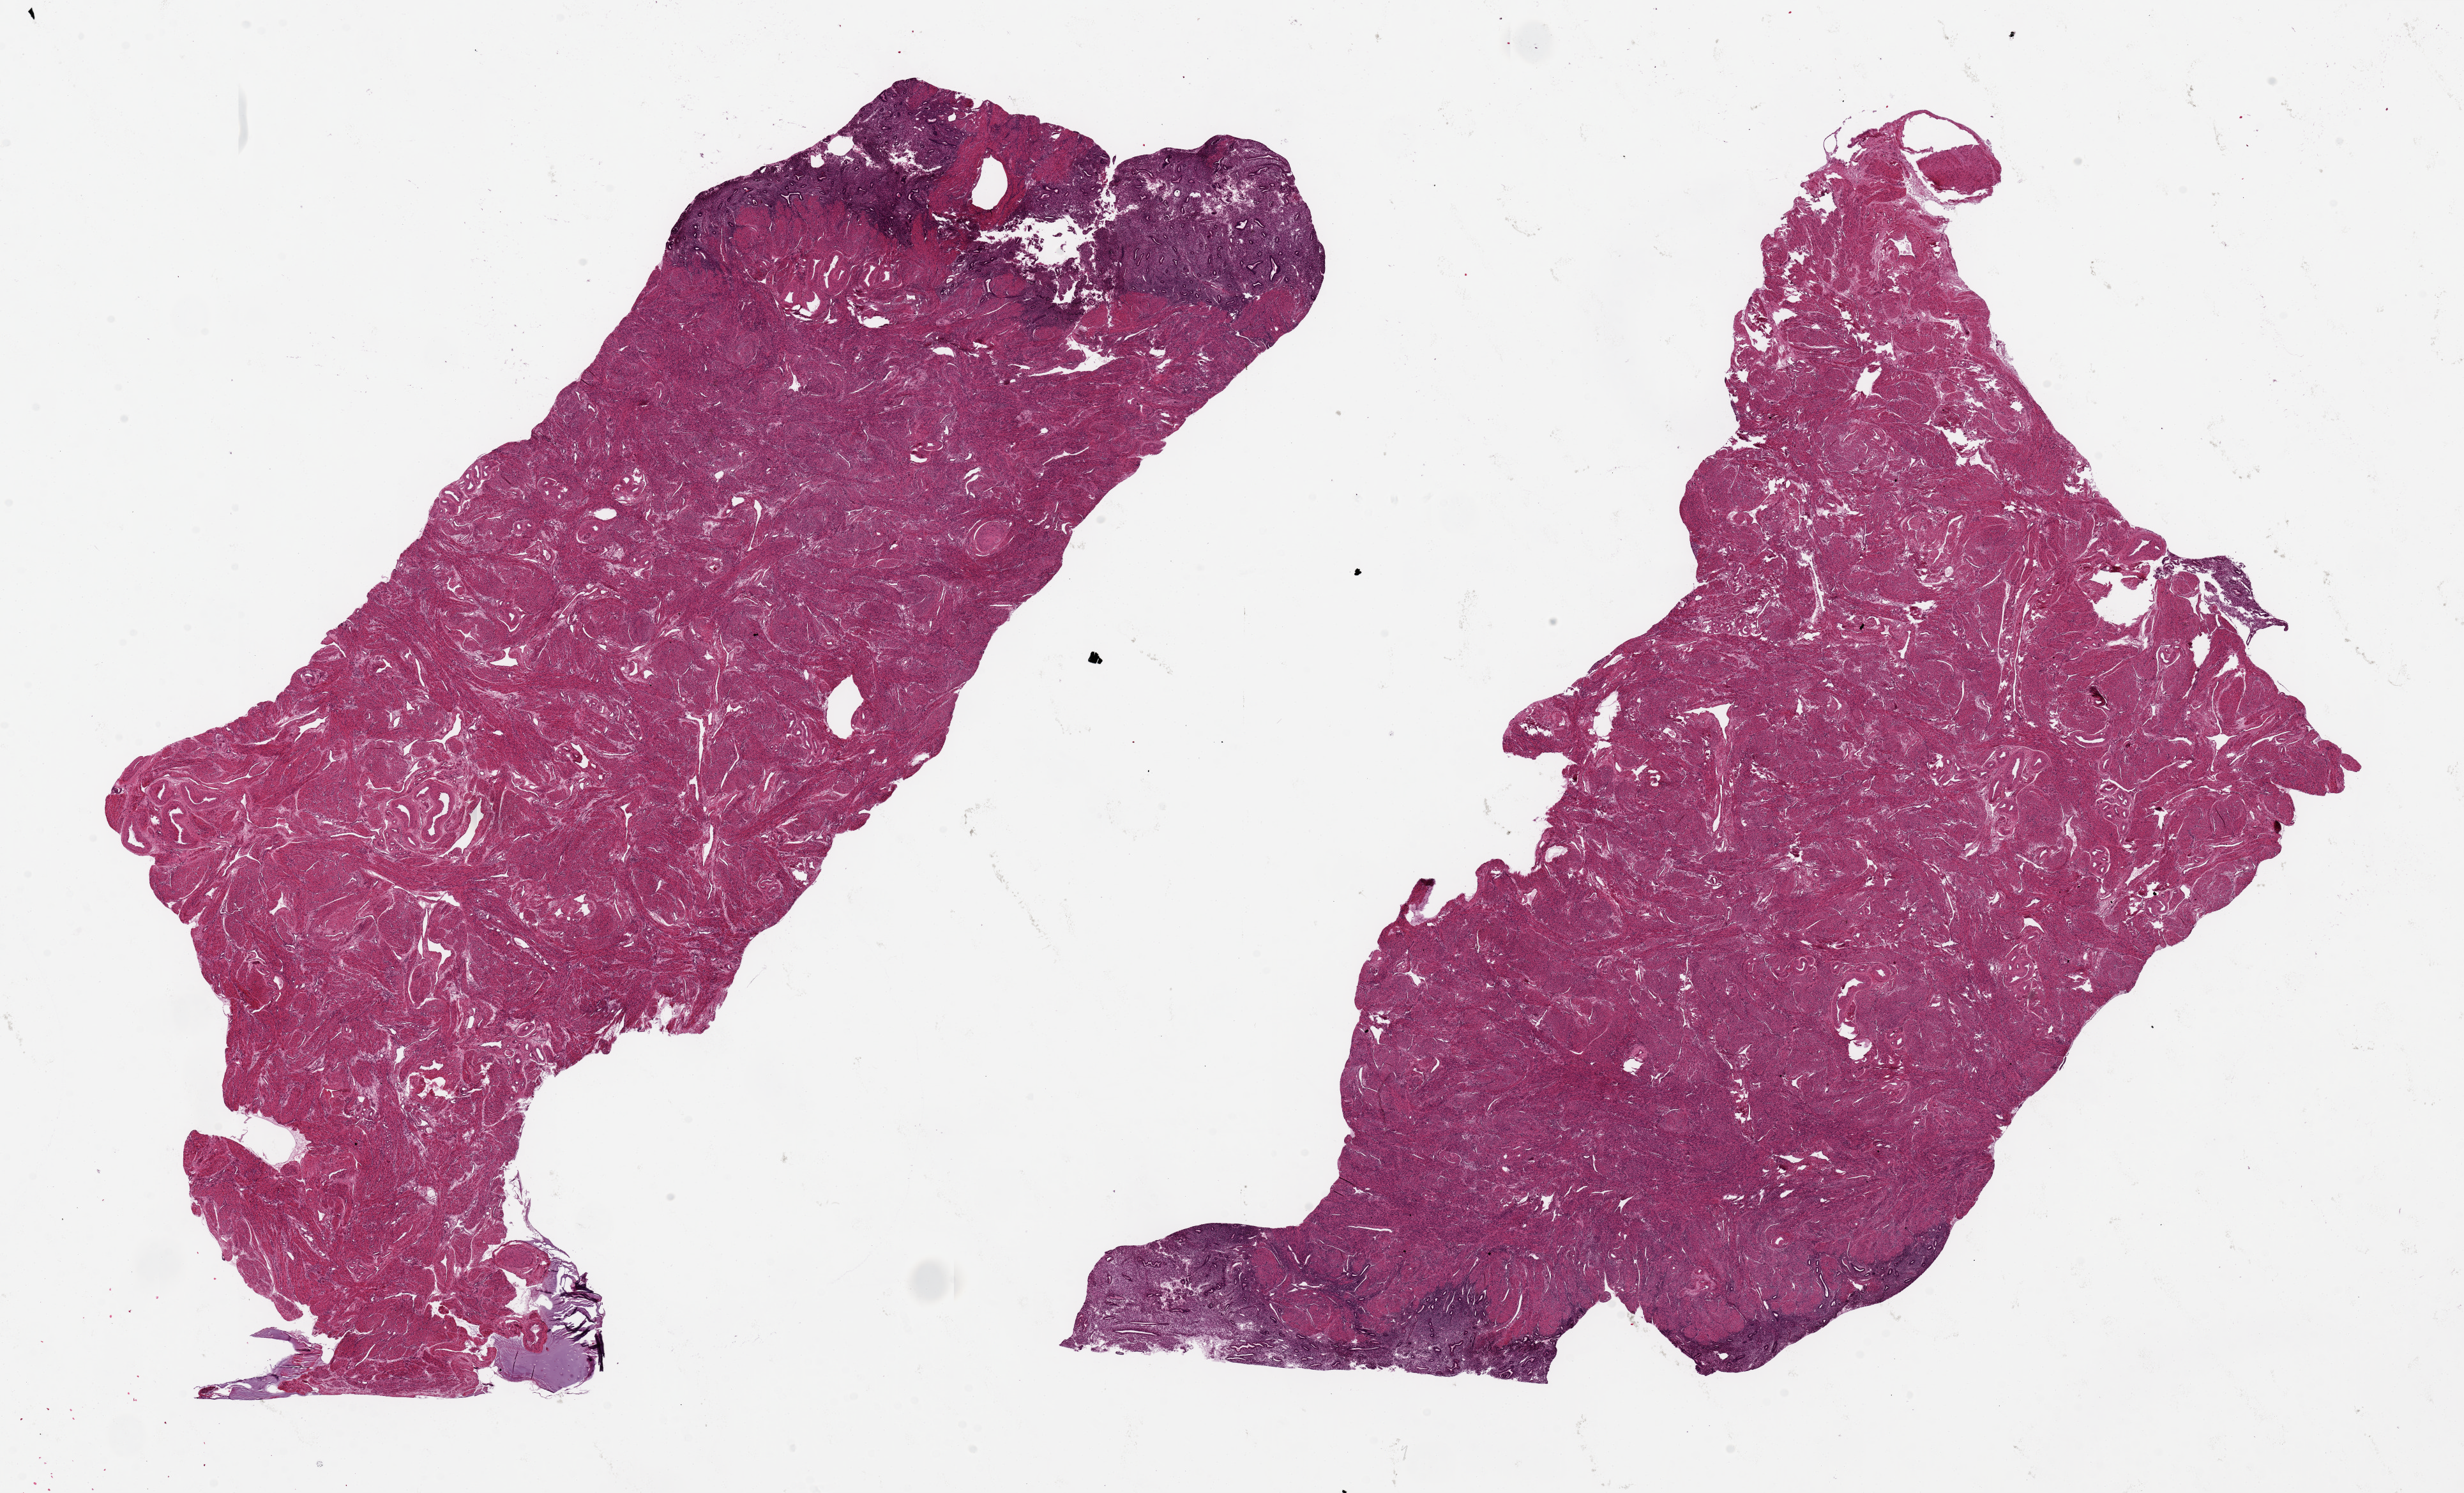
Digitized haematoxylin and eosin-stained section, shown as a low-resolution overview of the whole scanned area (about 30.5 x 18.5 mm); PAXgene-fixed, paraffin-embedded tissue; section of uterus (target tissue); tissue donor sample. Female donor.
Pathologist's review note for this sample: 2 pieces ~10x7mm, Scanty proliferative pattern endometrium, reasonably well preserved, up to 2 mm thick on edge of alqiuot.